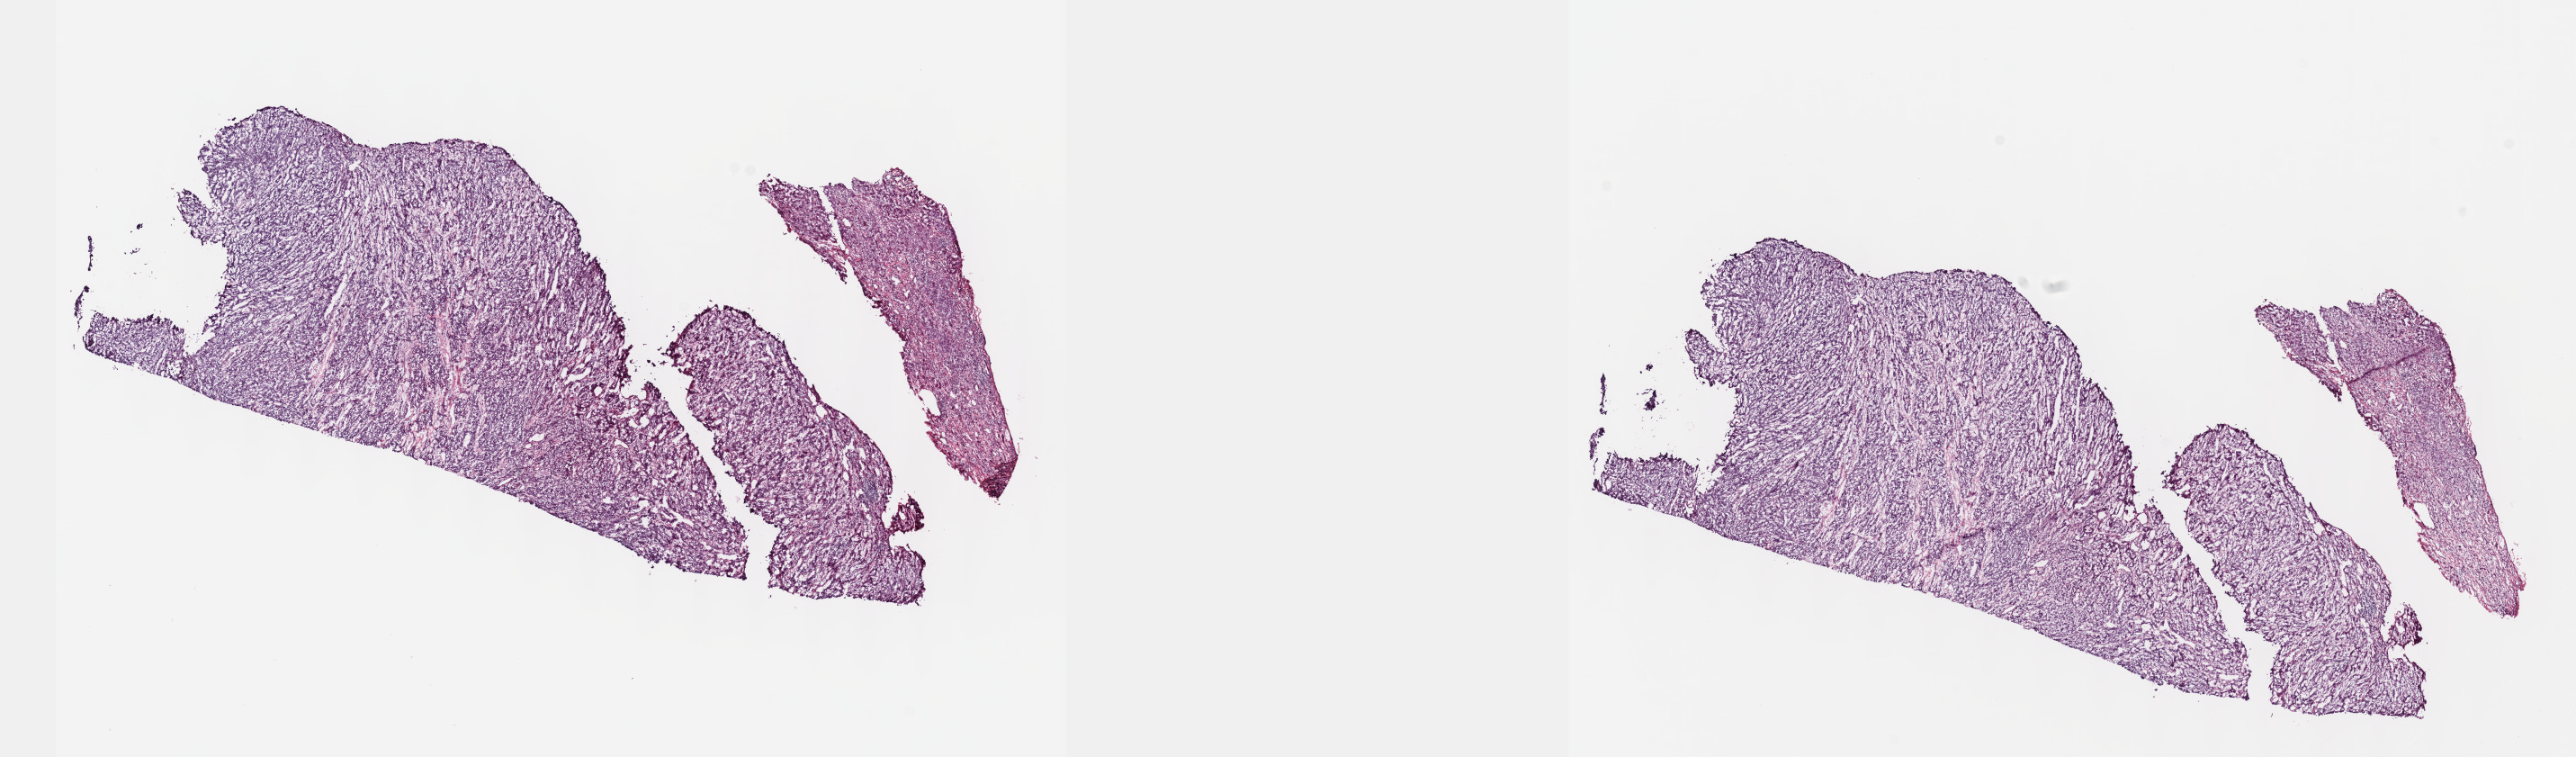
H&E whole-slide image, whole scanned area (about 23.1 x 6.8 mm, acquisition: 40x scan) shown as a low-resolution overview; frozen section from the top of the tissue portion; sample: primary tumour, liver. Female patient; age at initial diagnosis 60 years. Histologic grade: G3 (poorly differentiated). Composition of this section per pathologist review: tumour cells 80%, tumour nuclei 80%, normal cells 0%, stromal cells 20%, necrosis 0%. Infiltration values recorded for this section: lymphocyte infiltration 2%, monocyte infiltration 1%, neutrophil infiltration 1%.
AJCC pathologic stage: I (7th edition). Pathologic diagnosis: Hepatocellular carcinoma, NOS.